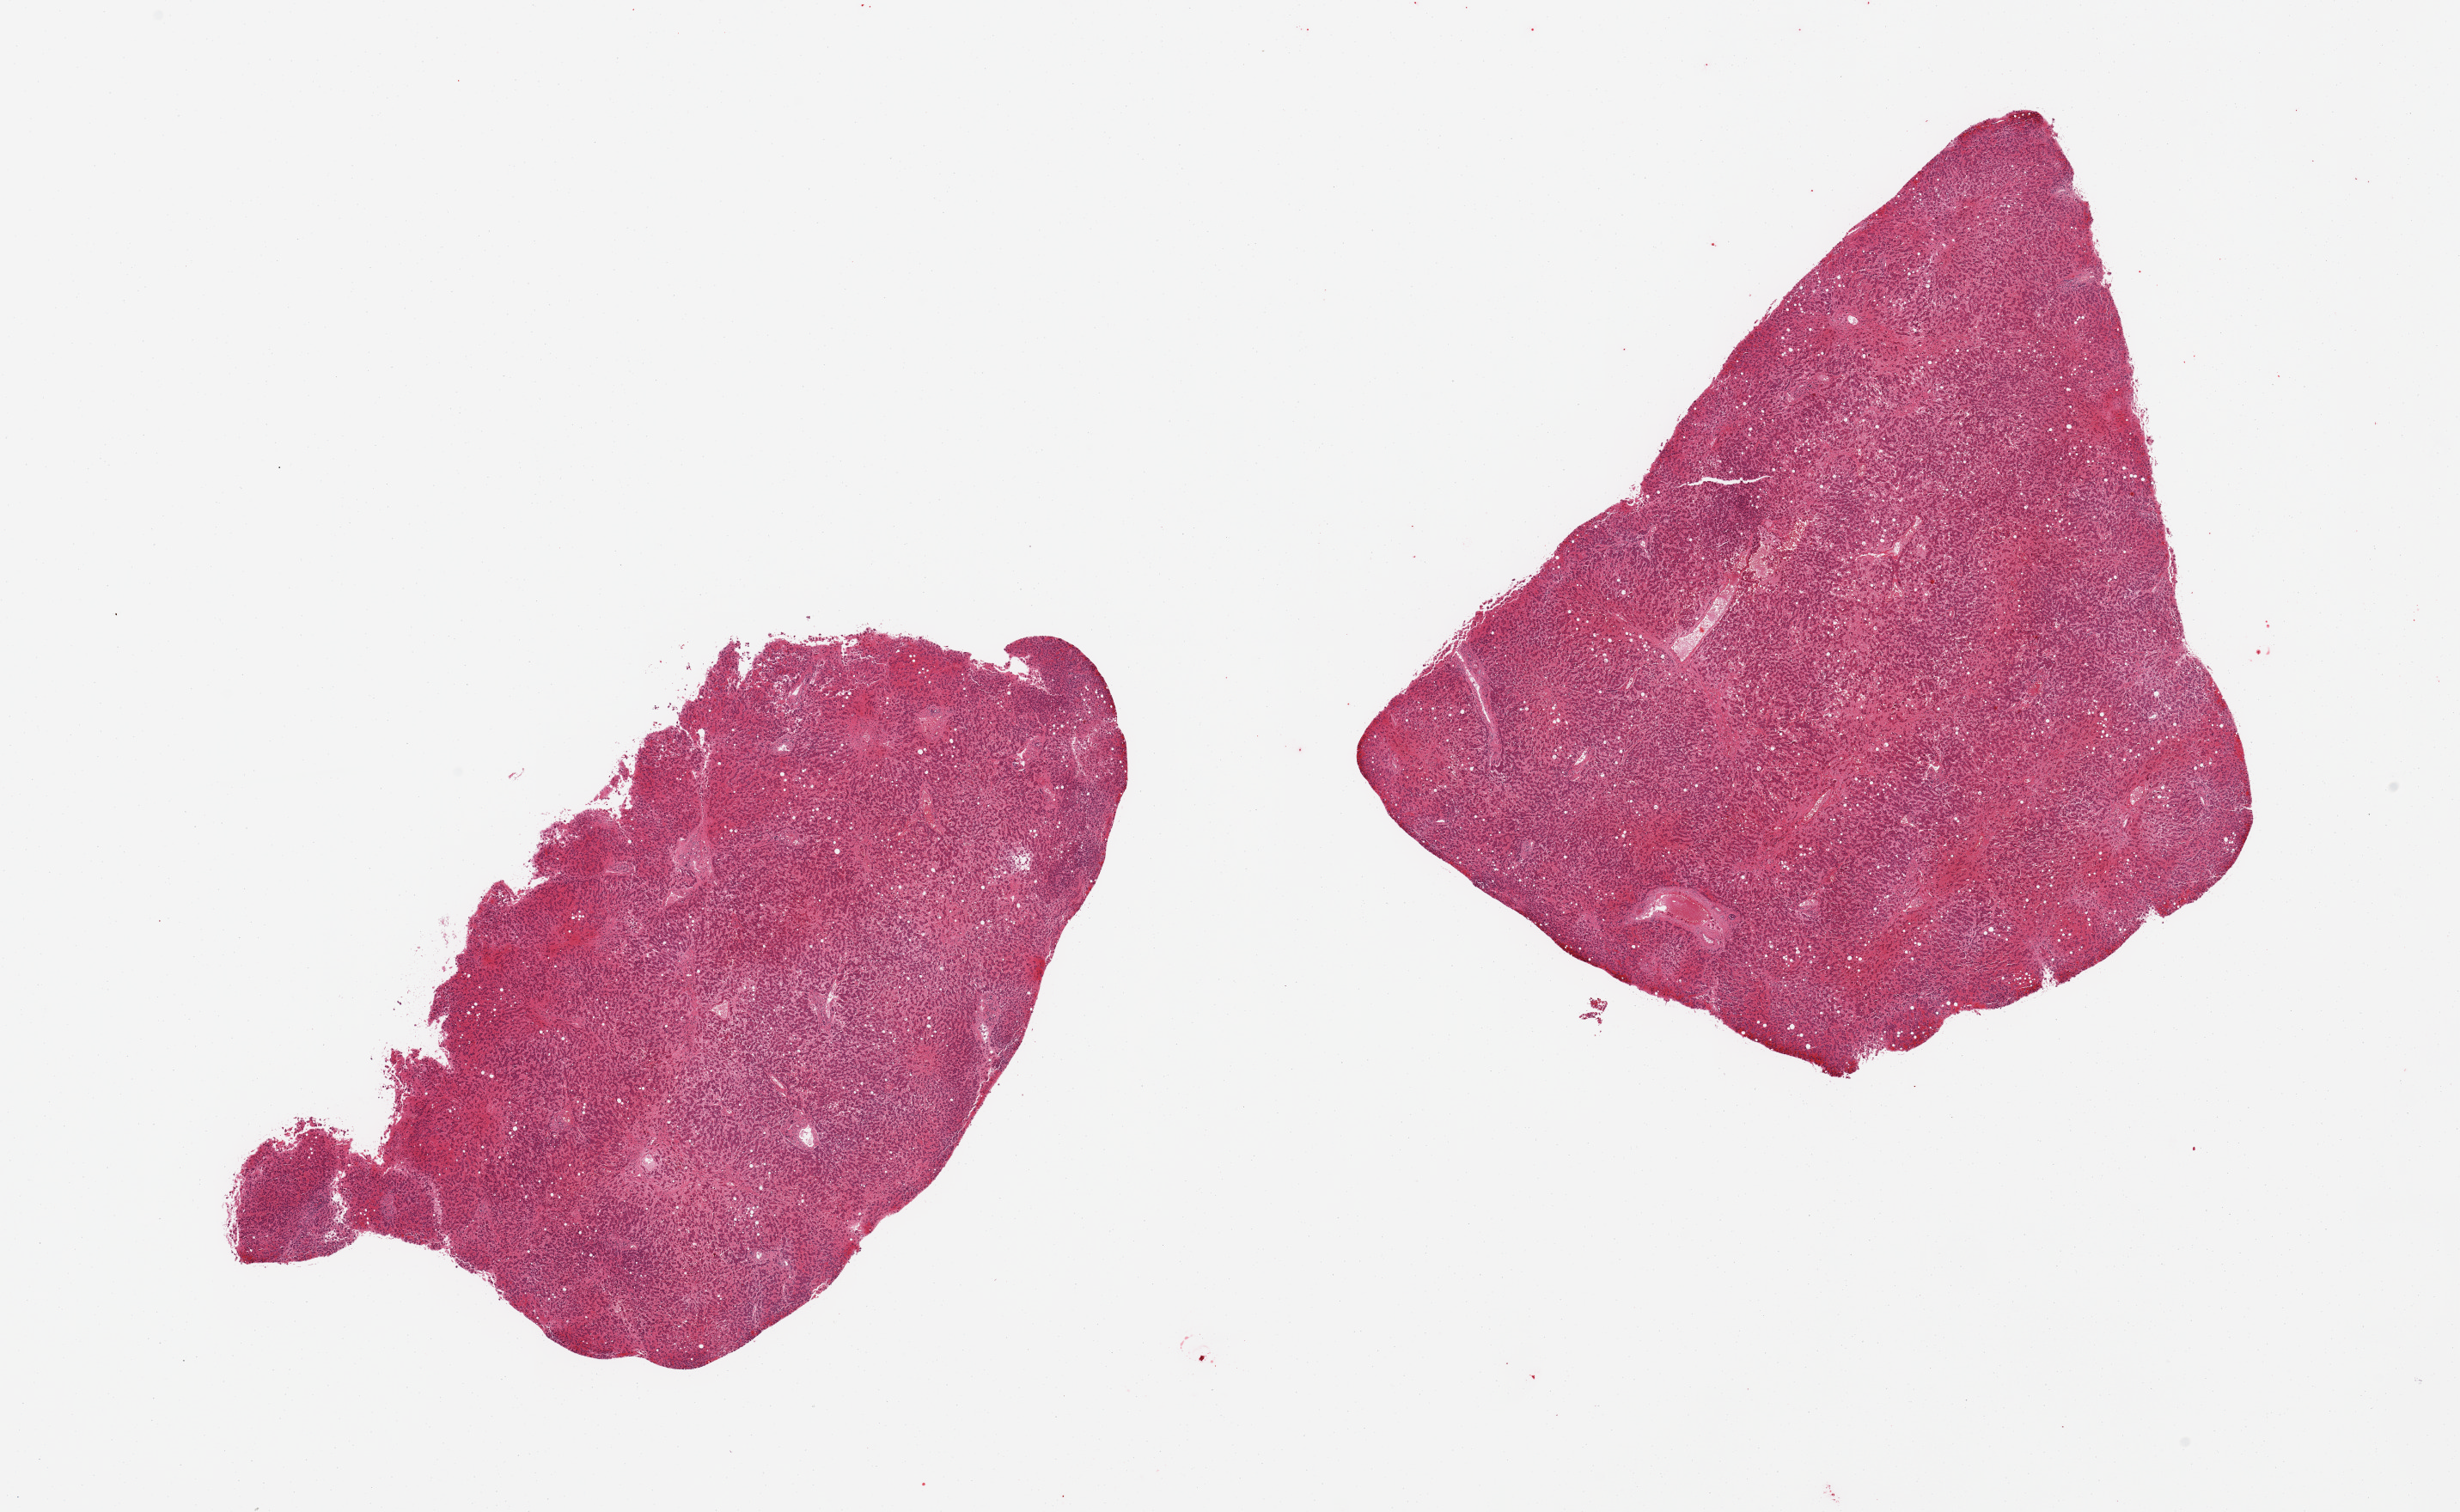
Digitized haematoxylin and eosin-stained section — whole scanned area (about 22.6 x 13.9 mm) shown as a low-resolution overview; PAXgene-fixed paraffin-embedded (PFPE) section; target tissue: liver; donor tissue sample. Female donor.
Reviewer comment on this tissue sample: 2 pieces; severe congestion; mild steatosis.